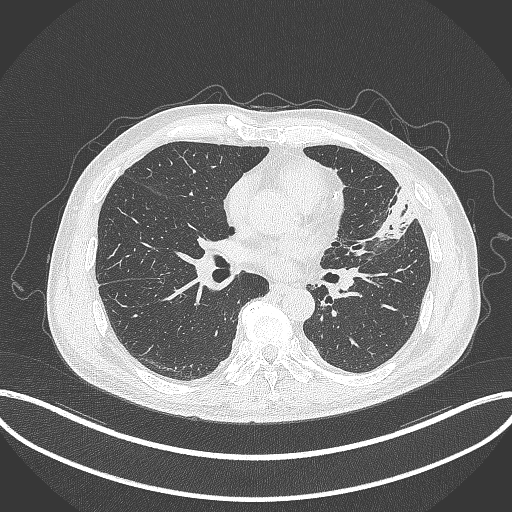
Chest CT, one axial slice; reconstruction kernel B70f; lung window (W 1500 / L -600 HU); 1 mm slice thickness; 512 × 512 image matrix, field of view 415 × 415 mm. Patient: male, 64 years. Case-level facts recorded for this patient, not image findings: clinical TNM (as recorded): T4 N1 M0; histopathological grade: G3.
Outlined on this slice (rectangle marked by the reading radiologist):
- lung tumour (recorded histology: adenocarcinoma): bounding box (x1, y1, x2, y2) in pixels: (362, 180, 422, 243)